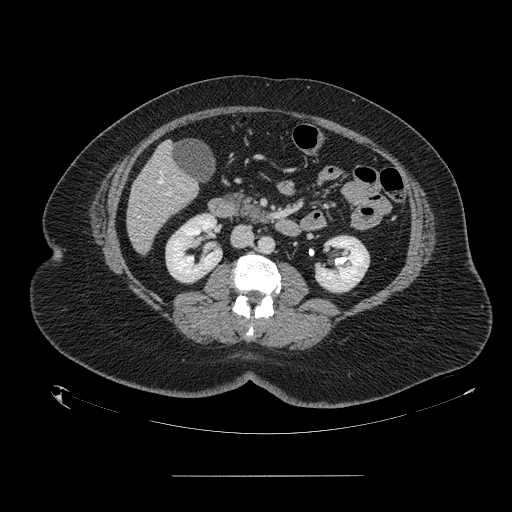
Contrast-enhanced abdominal CT, one axial slice. Position 52 of 164 along the scan axis. 120 kVp. Intravenous contrast given. Soft-tissue window (W 400 / L 40 HU). 512 × 512 image matrix, field of view 495 × 495 mm. Female patient, age 52 years. From the clinical record (not read from this slice): diagnosis: colorectal cancer liver metastases, imaged before liver resection; multiple liver metastases: yes; largest metastasis: 3.5 cm; chemotherapy before resection: no.
Structures marked on this image (expert manual segmentation):
- hepatic veins: bounding box [x1, y1, x2, y2] px = [138, 172, 174, 217]
- liver: [127, 144, 198, 252]
- portal vein (with intrahepatic branches): [165, 193, 169, 196]